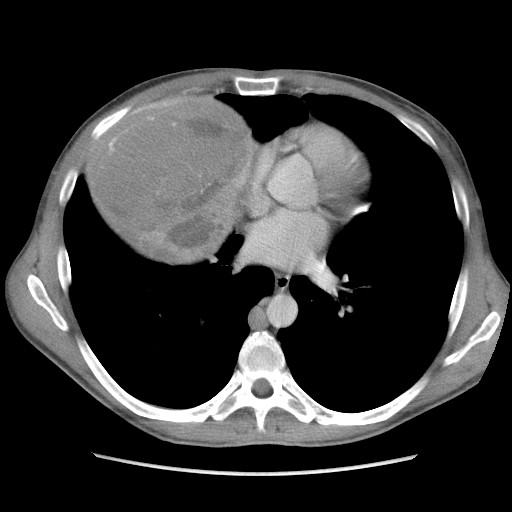
Contrast-enhanced abdominal CT, one axial slice; slice 101 of 115 in the series (ordered by position); soft-tissue window (W 400 / L 40 HU); 5 mm slice thickness; 512 × 512 image matrix. Male patient. Case-level facts recorded for this patient, not image findings: diagnosis: adrenocortical carcinoma; tumour side: right adrenal; Ki-67 index: 13 %; stage (as recorded): 3.
Structures marked on this image (semi-automatically segmented with operator editing):
- mass: box from (x=95, y=96) to (x=251, y=259) px